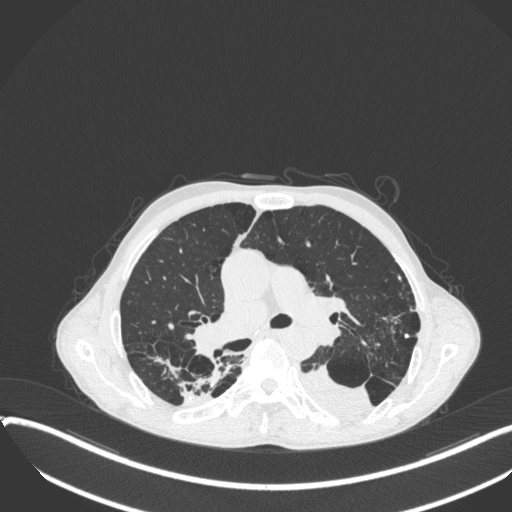
Chest CT, one axial slice. Position 235 of 400 along the scan axis. Reconstruction kernel B31f. 120 kVp. Lung window (W 1500 / L -600 HU). 512 × 512 image matrix, field of view 400 × 400 mm. Patient: male, 57 years. From the clinical record (not read from this slice): clinical TNM (as recorded): T4 N0 M0.
Structures marked on this image (rectangle marked by the reading radiologist):
- lung tumour (recorded histology: squamous cell carcinoma): bounding box [x1, y1, x2, y2] px = [297, 357, 377, 420]